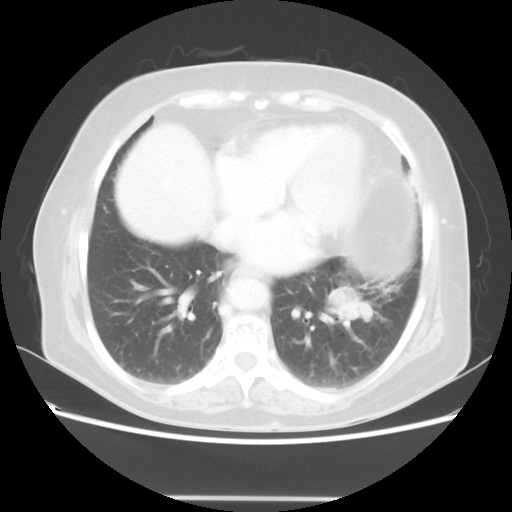
Chest CT, one axial slice; slice 21 of 56 in the series (ordered by position); 100 kVp; lung window (W 1500 / L -600 HU); 5 mm slice thickness; 512 × 512 image matrix, field of view 360 × 360 mm. Female patient, age 73 years. From the clinical record (not read from this slice): clinical TNM (as recorded): T1c N0 M0.
Annotated regions visible in this slice (bounding box drawn by a radiologist):
- lung tumour (recorded histology: adenocarcinoma): bounding box (x1, y1, x2, y2) in pixels: (329, 283, 380, 333)